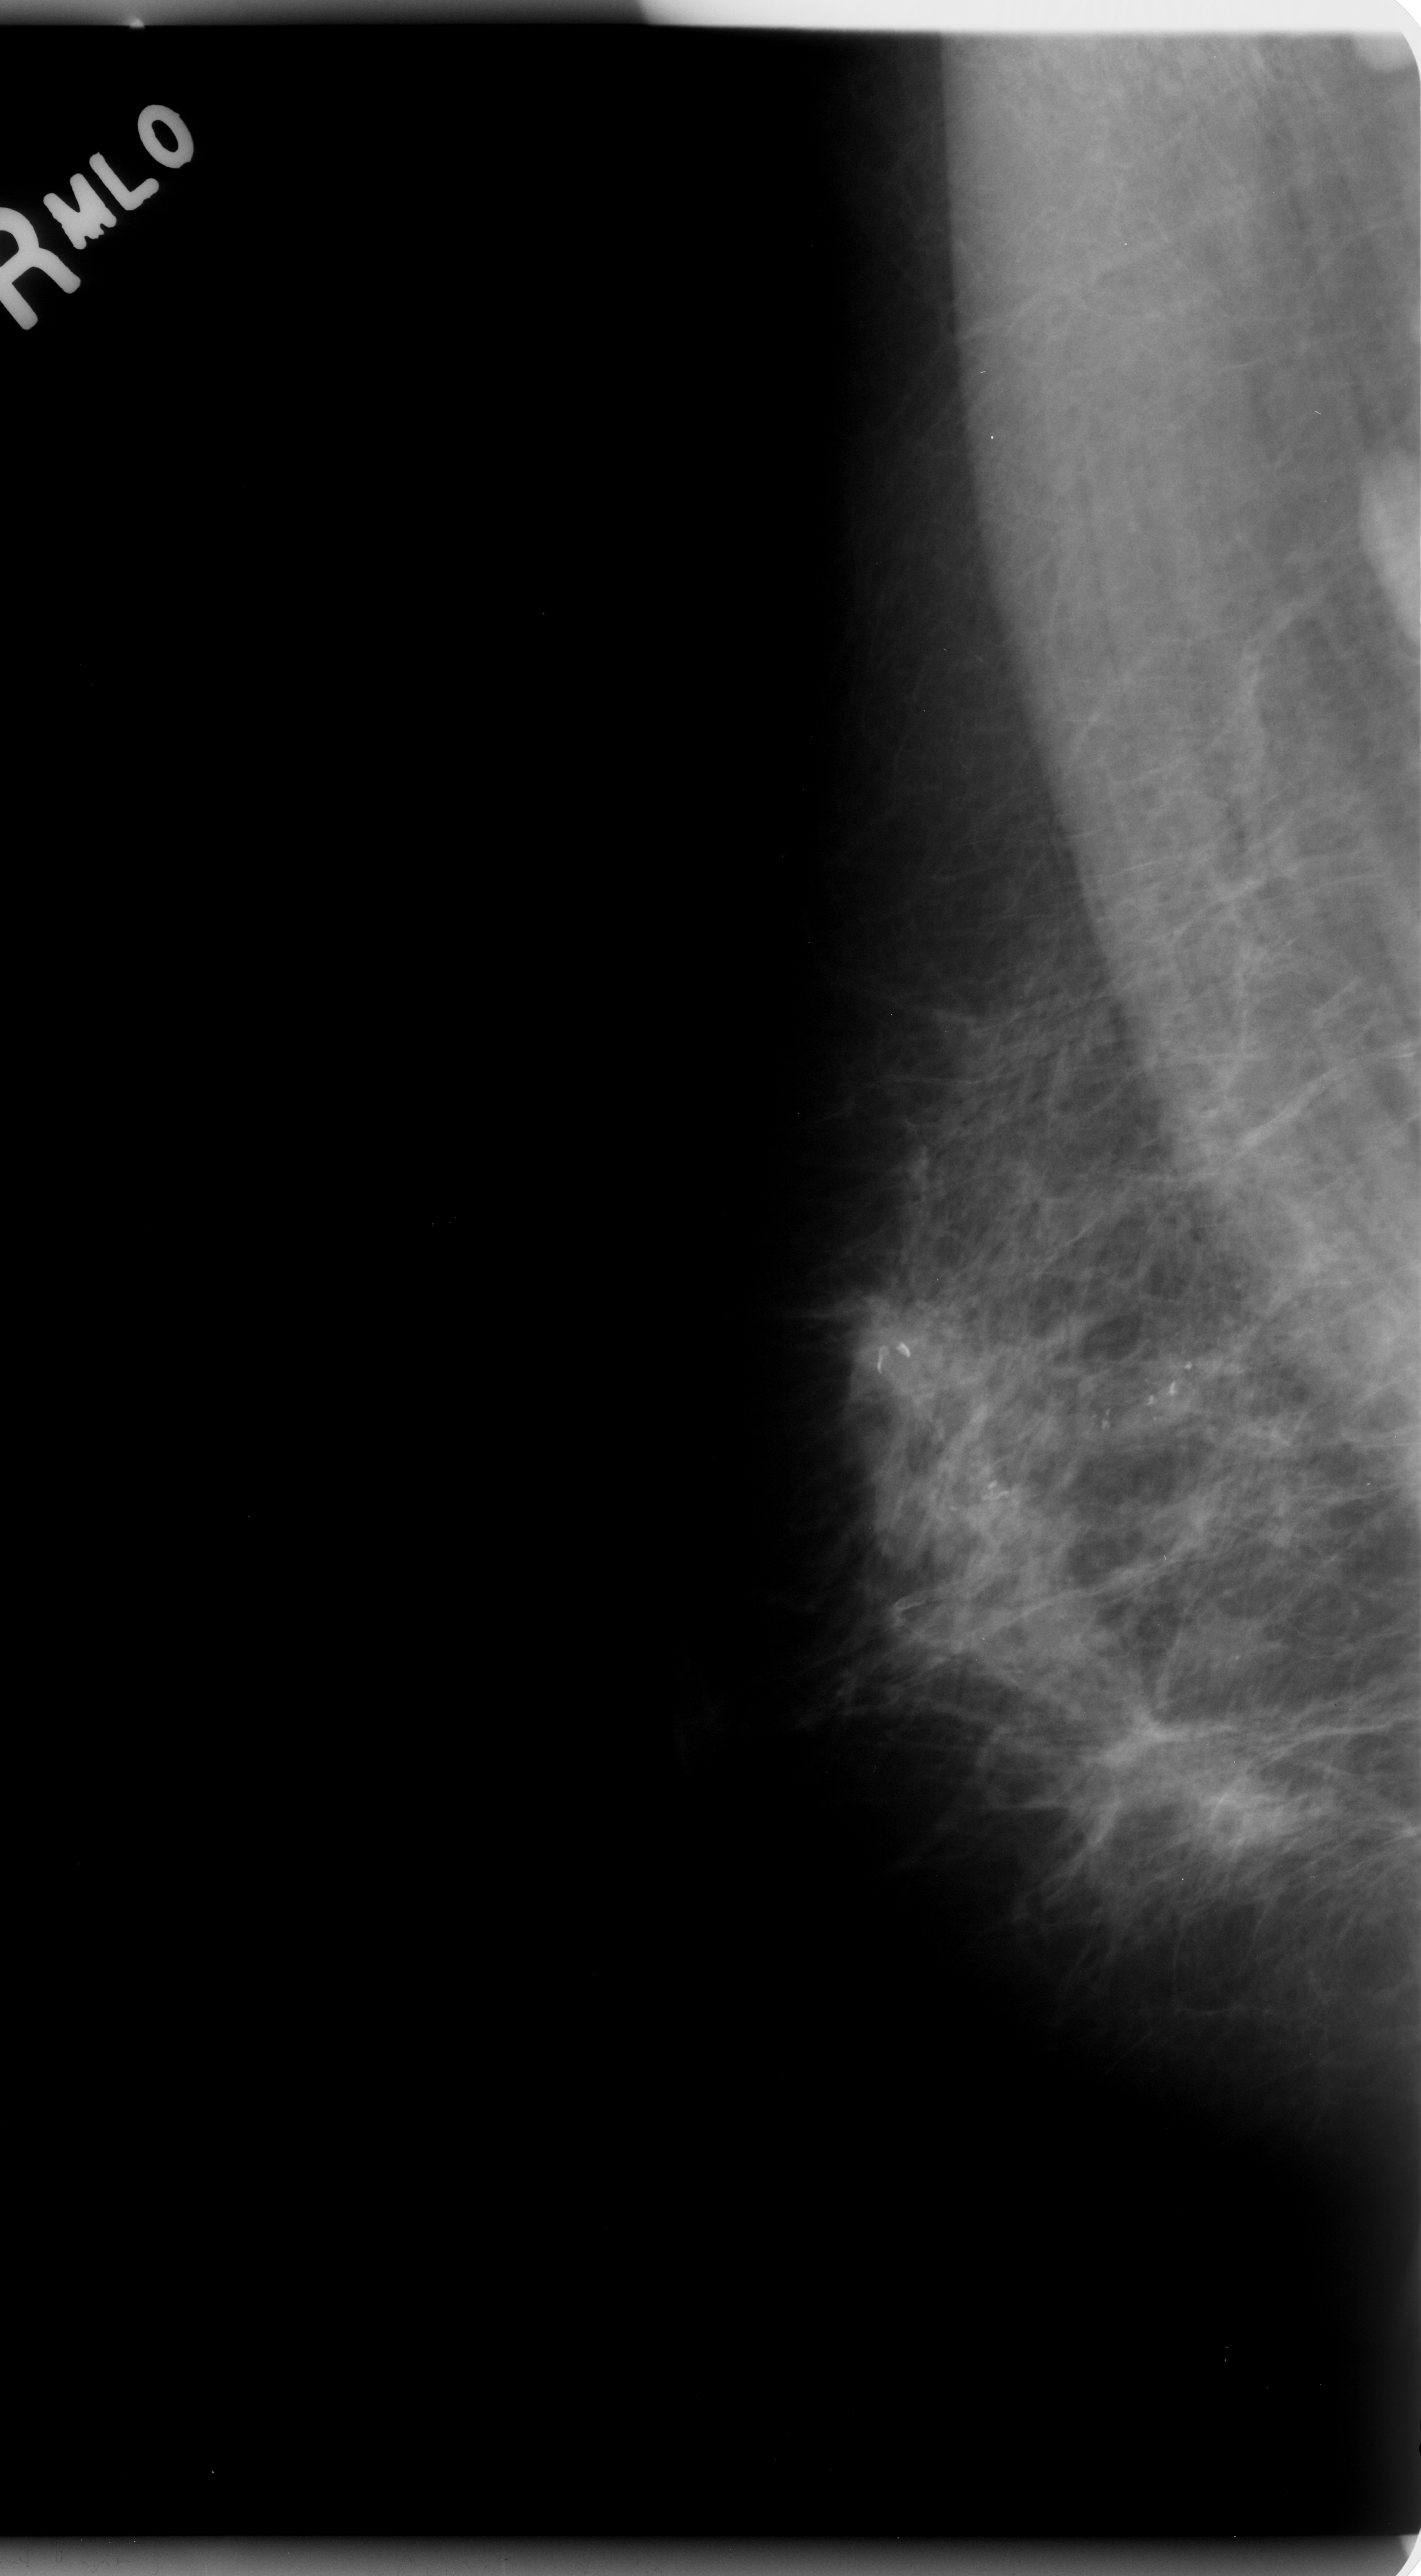
Mammogram (digitized film); right breast; mediolateral oblique (MLO) view; BI-RADS breast density category 2 (scale 1–4); 1421 × 2576 image matrix.
Marked abnormalities (boxes around the expert regions of interest):
- calcifications, morphology pleomorphic, distribution segmental; BI-RADS assessment category 5; pathology result (as recorded, not read from the image): malignant: bounding box <788,1242,1387,1579> (left, top, right, bottom; pixels)